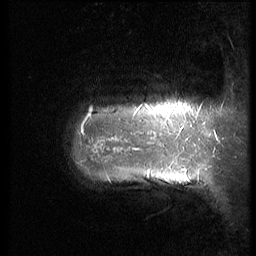
Breast MRI (dynamic contrast-enhanced), one sagittal slice. Position 7 of 64 along the scan axis. 3 images stored at this slice position (order not interpretable as contrast timing). 1.5 T. TE 4.2 ms, TR 9 ms. 256 × 256 image matrix, field of view 180 × 180 mm. Patient: female, 39 years. From the clinical record (not read from this slice): setting: breast cancer imaged before/during neoadjuvant chemotherapy; receptor status: HER2-positive.
Outlined on this slice (semi-automatically segmented with operator editing):
- analysis volume of interest (the breast-tissue region the enhancement analysis was run in; not a lesion): bounding box [x1, y1, x2, y2] px = [62, 67, 210, 220]
- tumour enhancement mask (voxels above the 140 % enhancement threshold inside the analysis volume of interest): [82, 104, 153, 157]